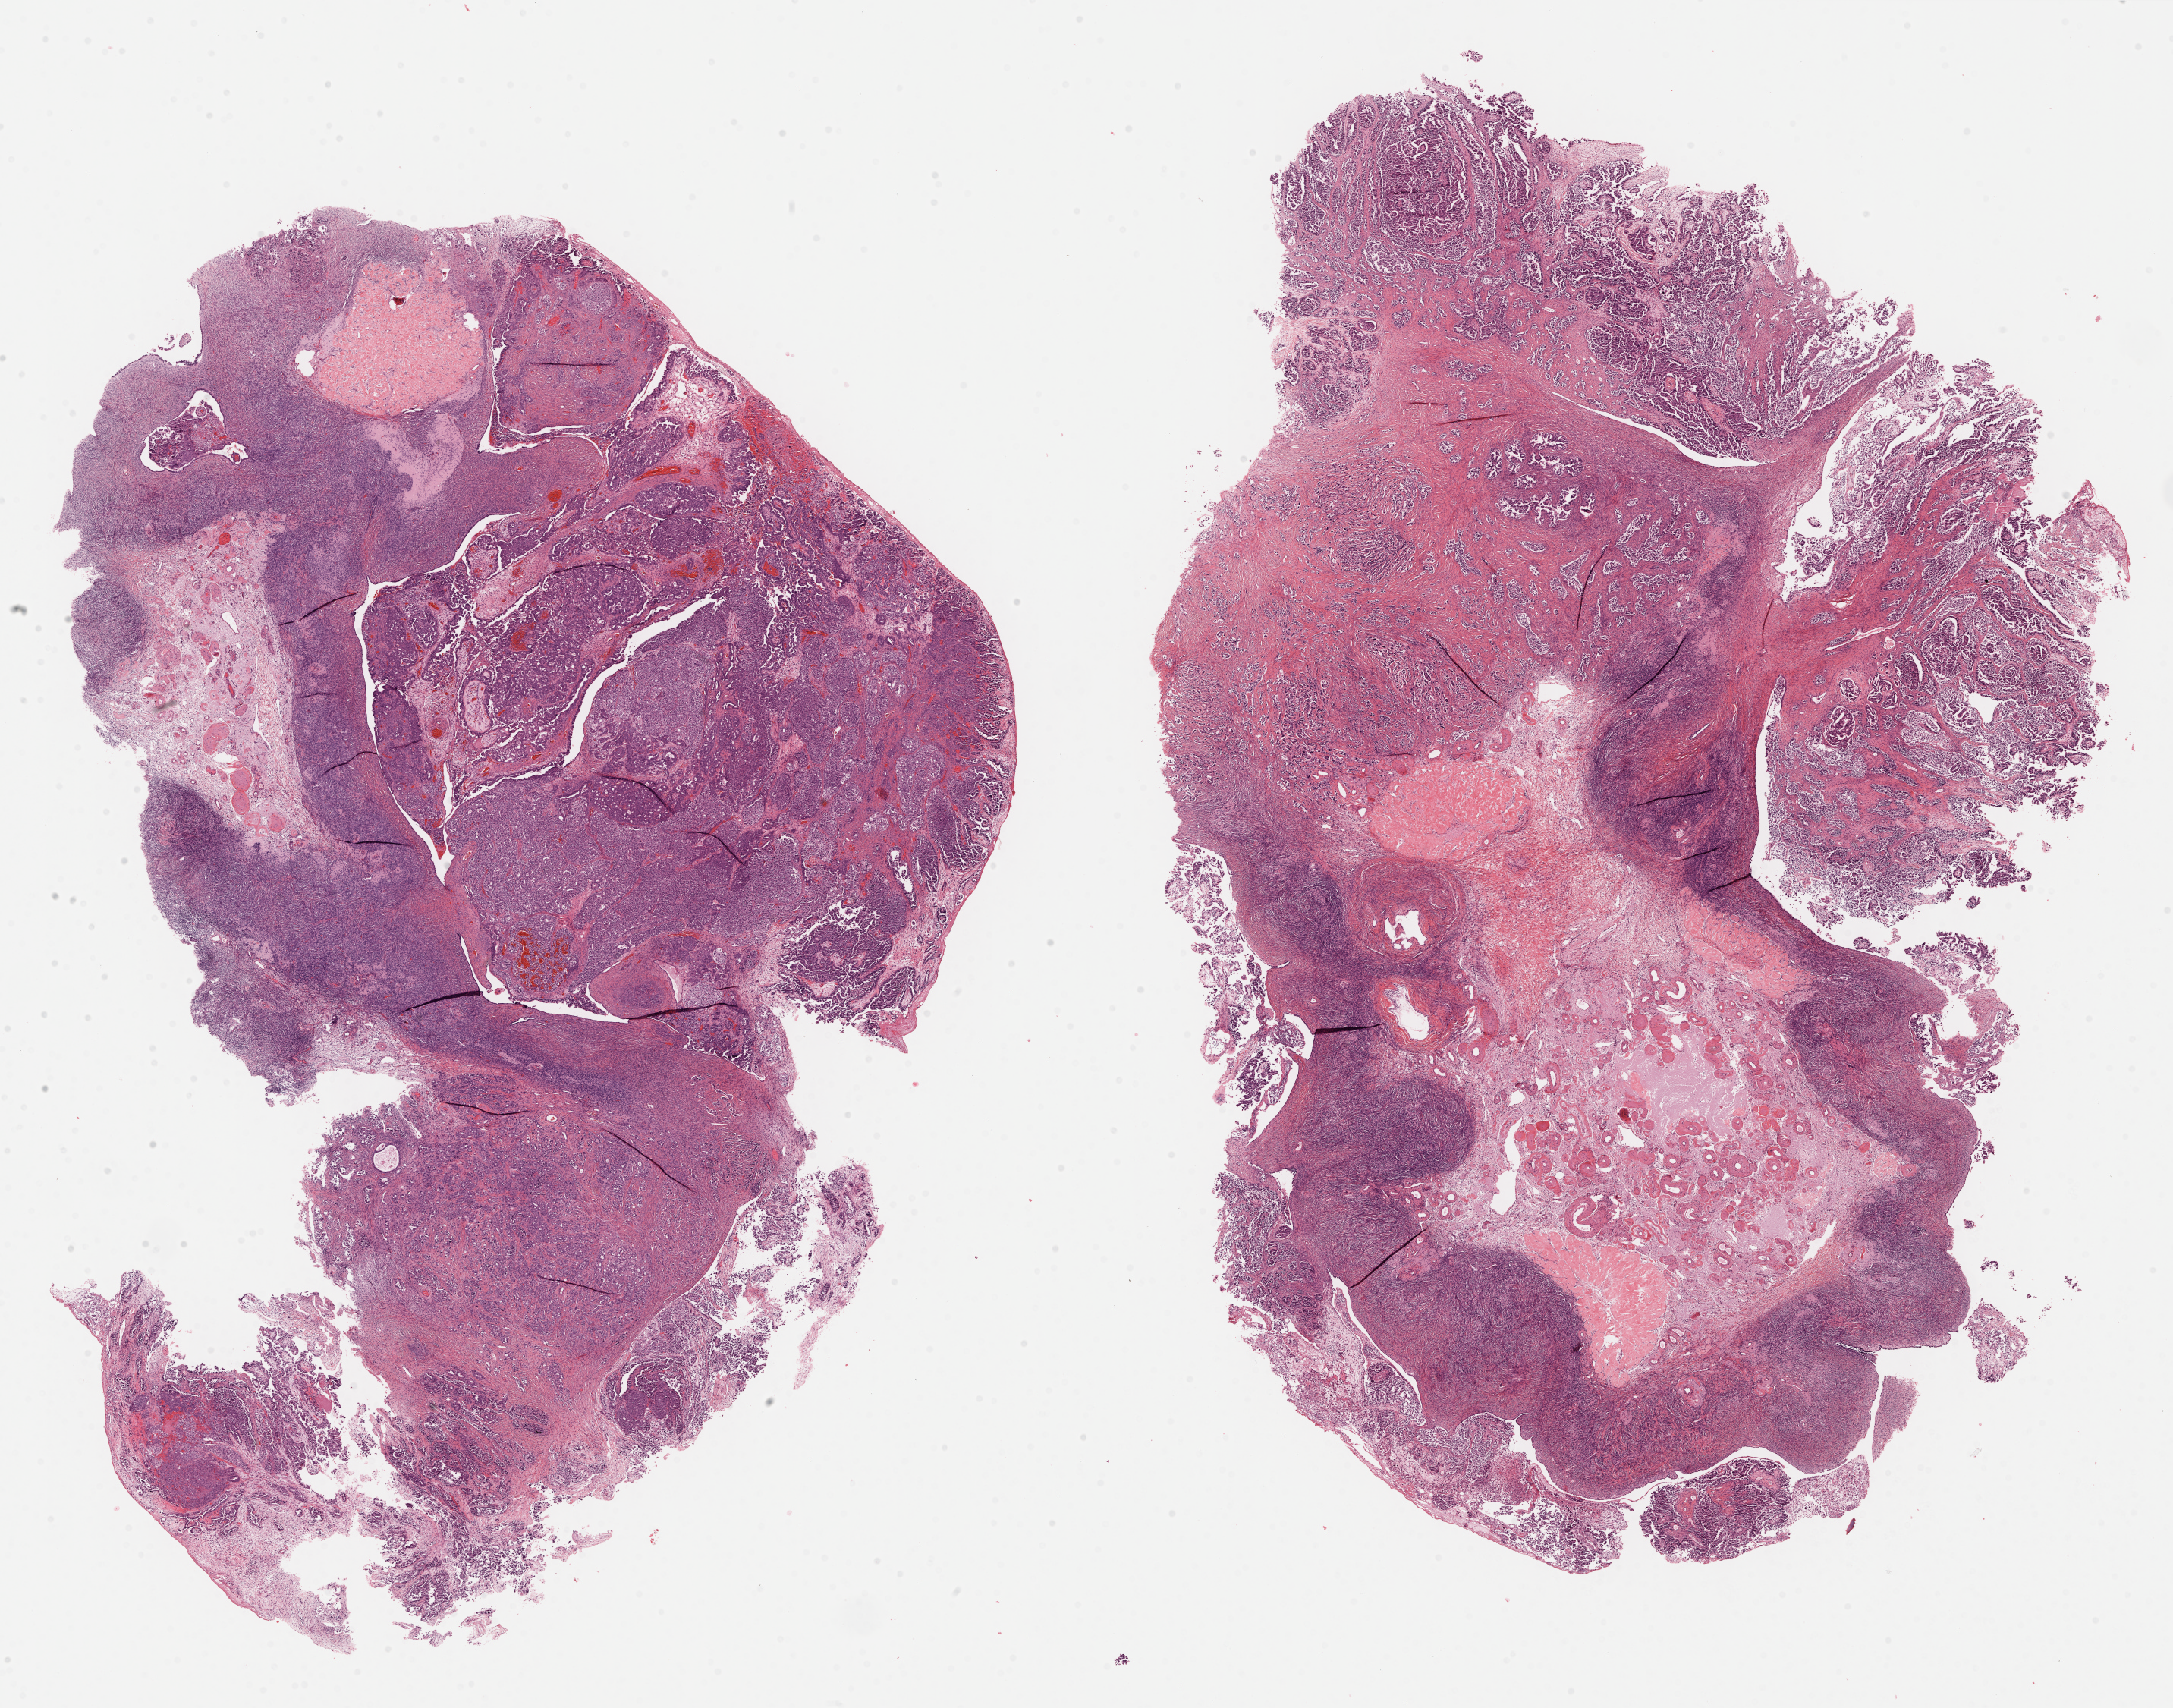
Digitized H&E tissue section (whole slide), a low-resolution overview of the entire scanned area, about 23.1 x 18.2 mm (slide scanned at 40x), formalin-fixed paraffin-embedded (FFPE) diagnostic section, primary tumour sample from the ovary. Female patient; age at initial diagnosis 66 years. Histologic grade: G3 (poorly differentiated).
* pathologic diagnosis: Serous cystadenocarcinoma, NOS
* FIGO stage: IIIC